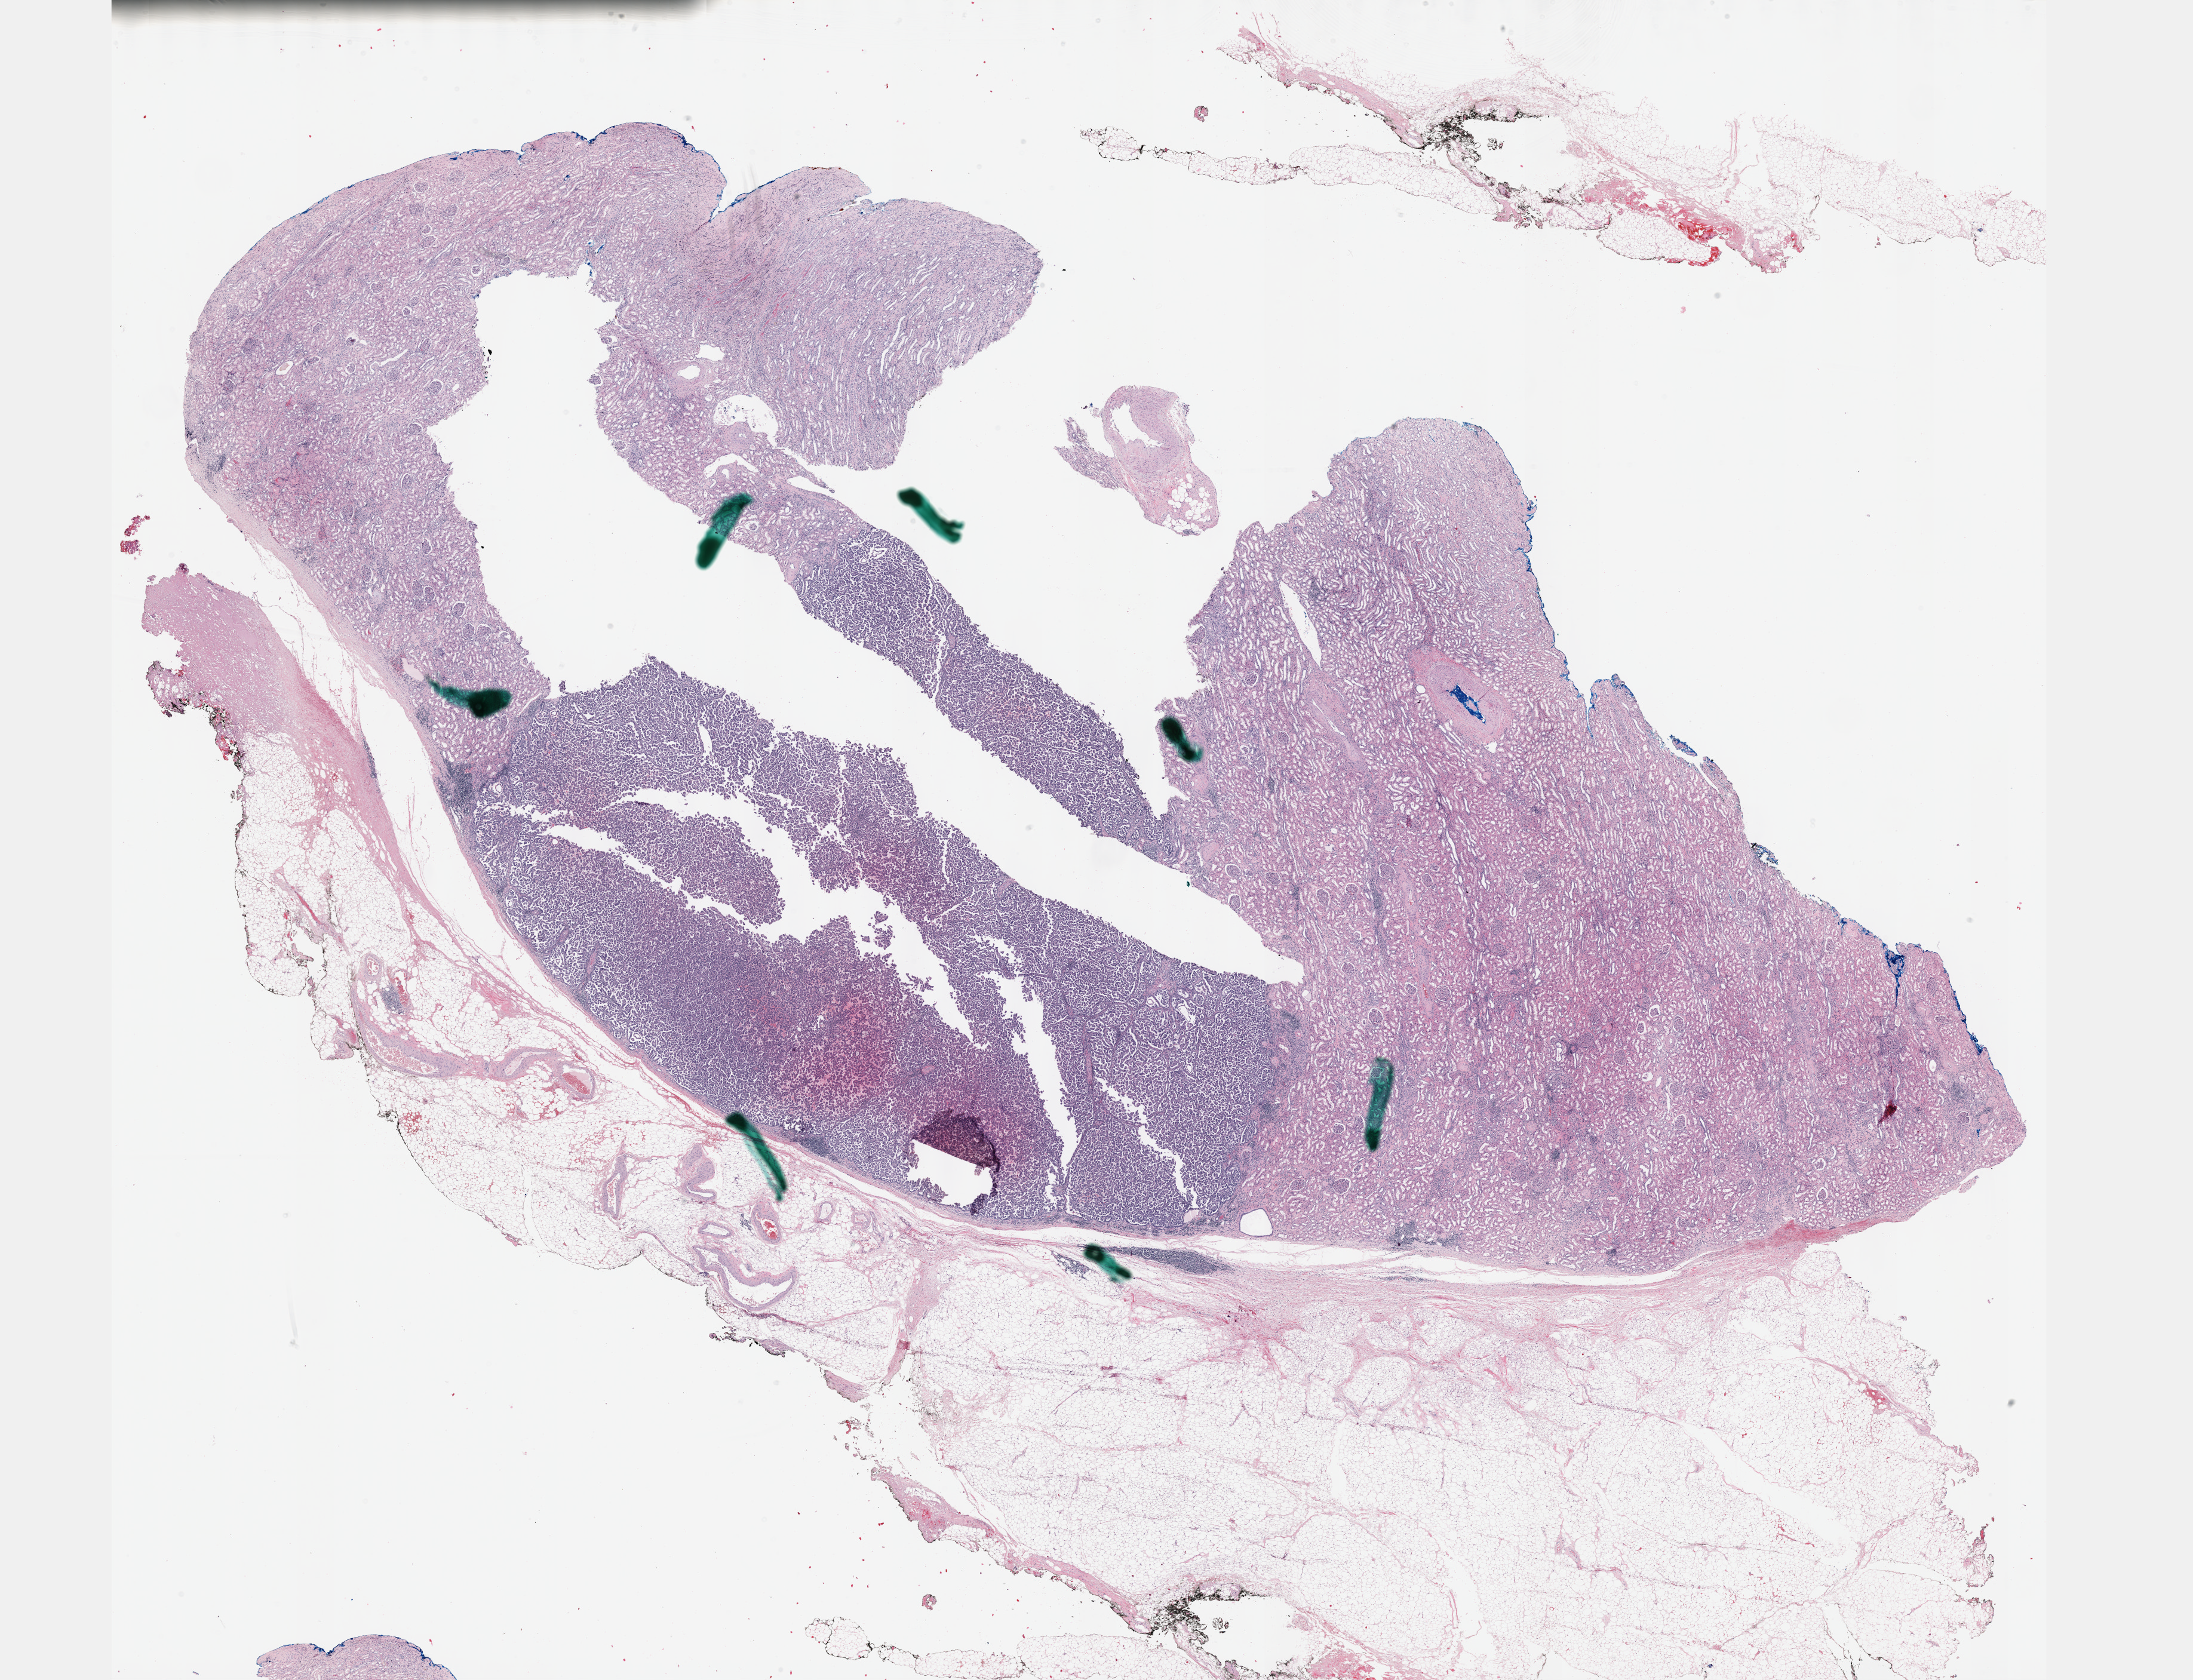
Digitized Hematoxylin and eosin (H&E) stained tissue section (whole slide) — whole scanned area (about 29.7 x 22.7 mm) shown as a low-resolution overview; FFPE section; primary tumour sample from the kidney. Male patient; age at initial diagnosis 65 years.
AJCC pathologic stage: I (7th edition). Pathologic diagnosis: Papillary adenocarcinoma, NOS.